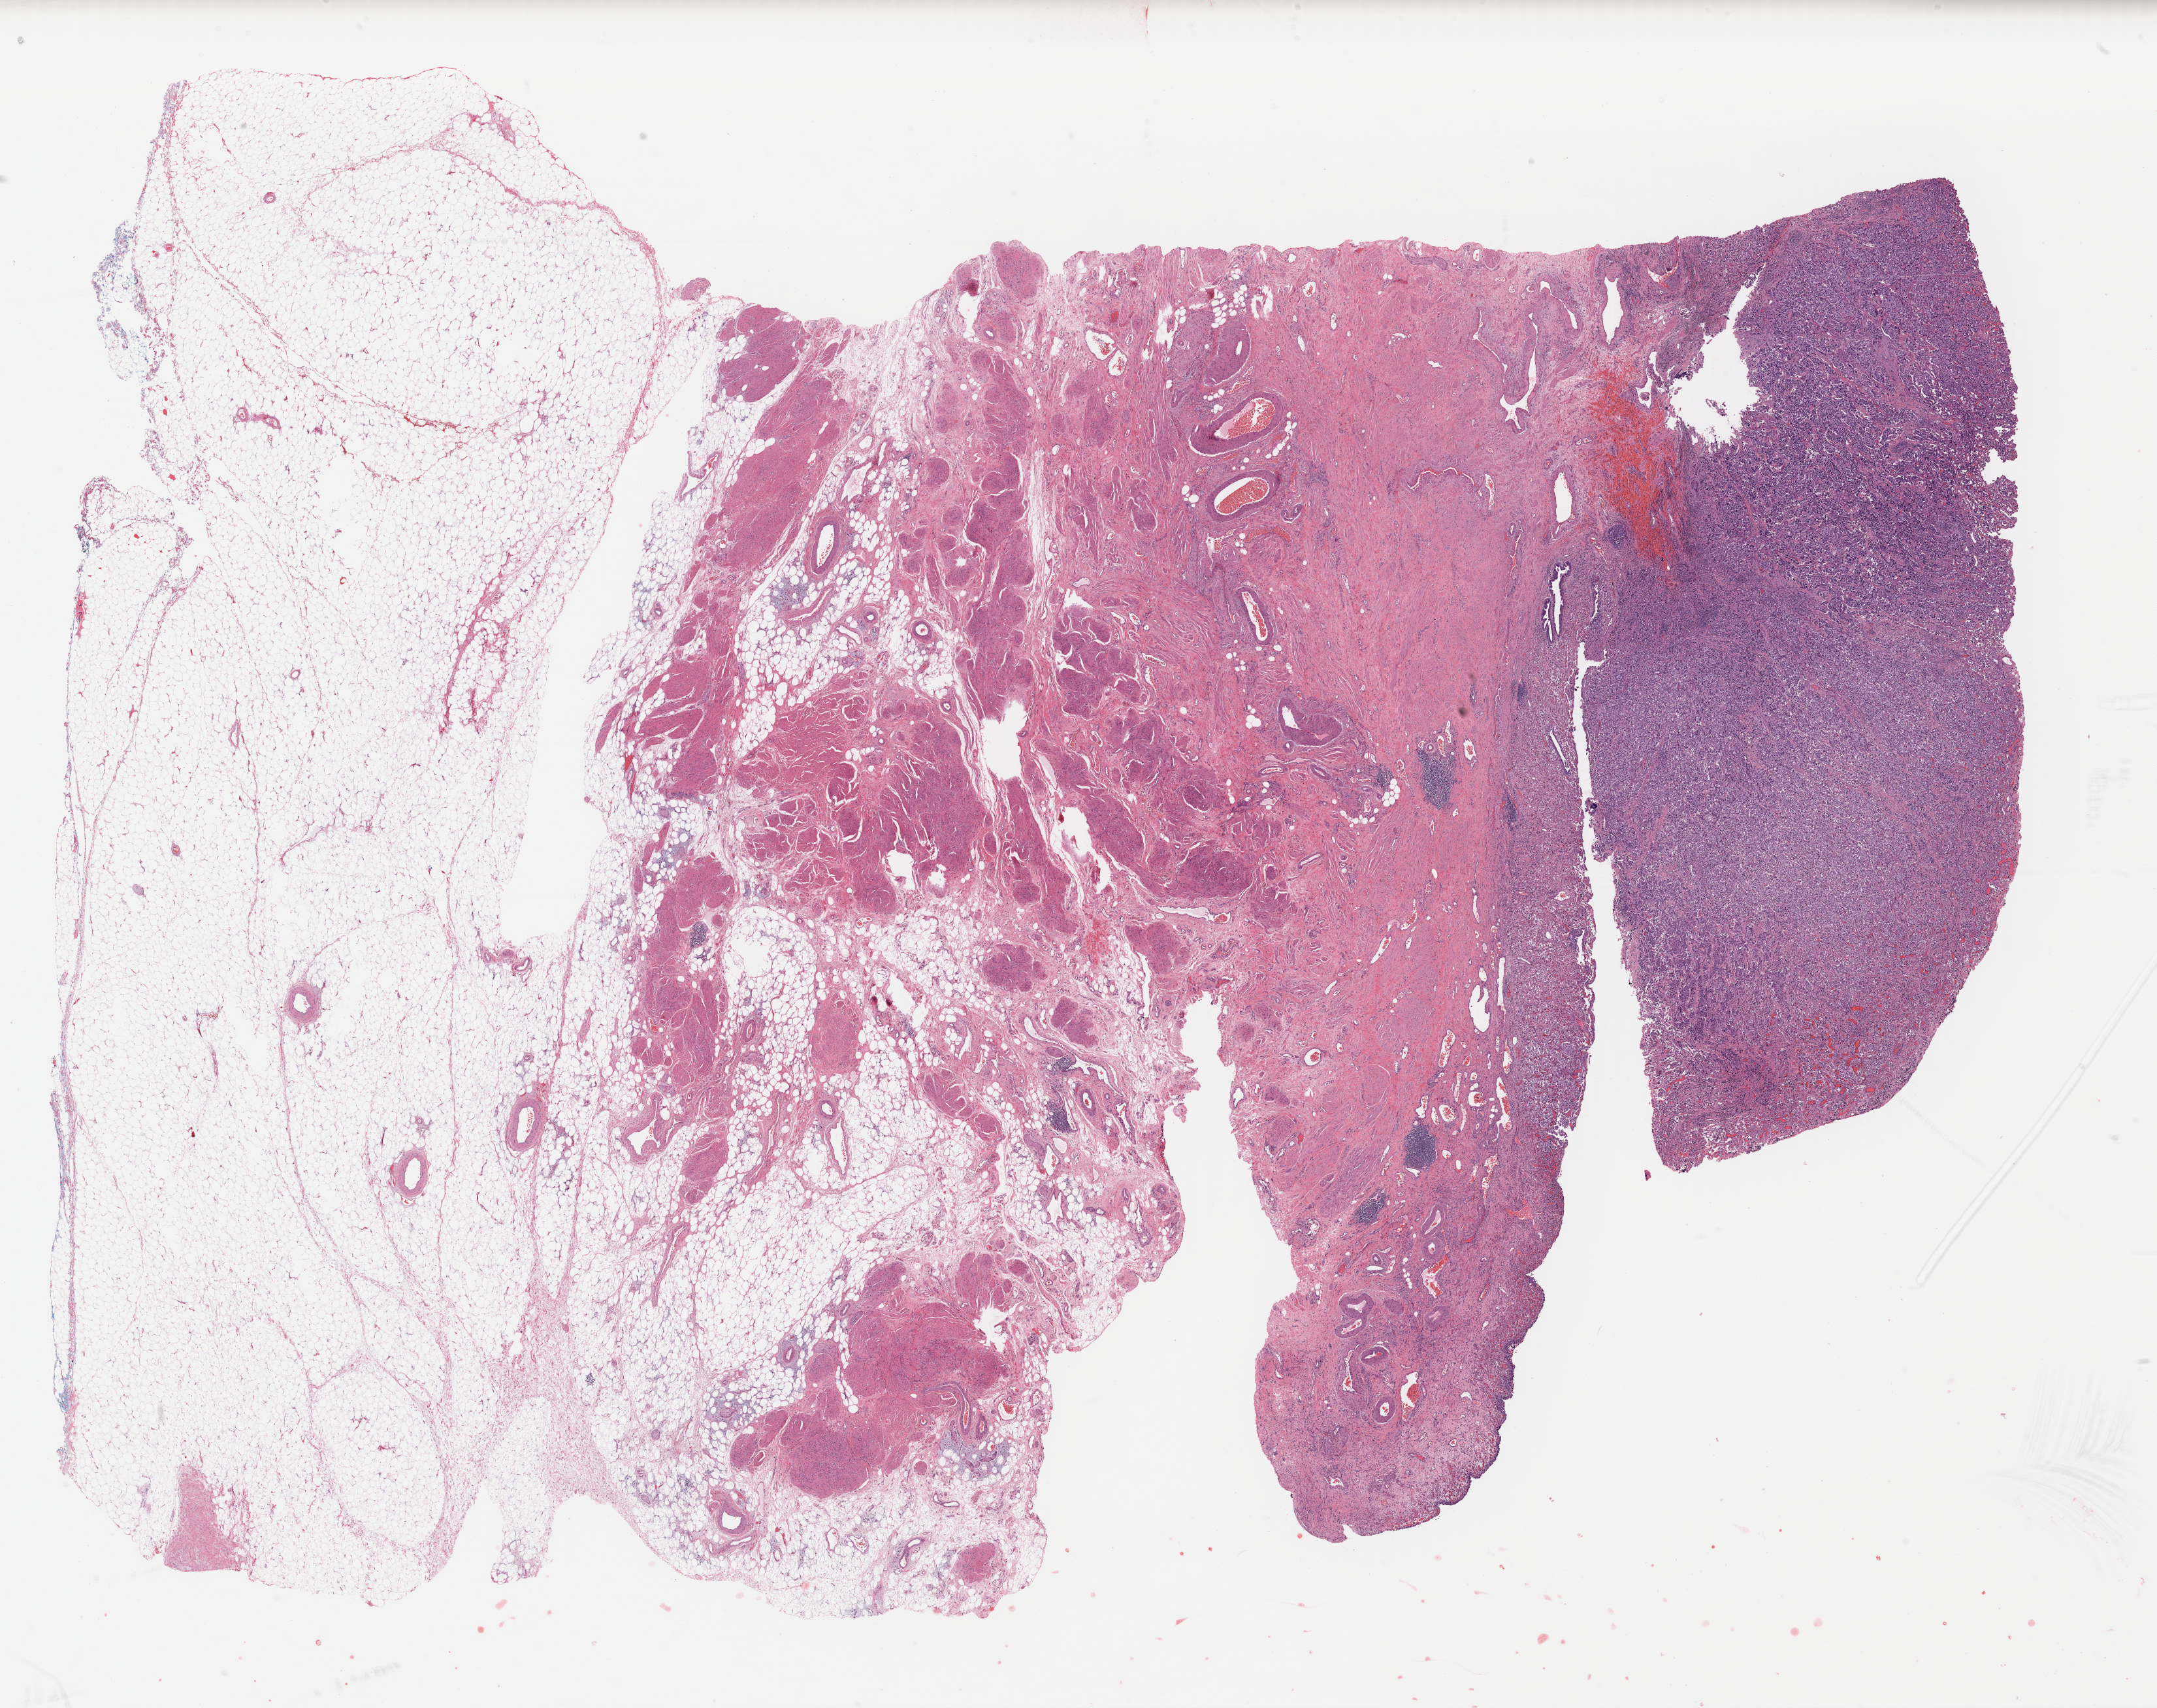
Digitized H&E-stained tissue section (whole slide) — shown as a low-resolution overview of the whole scanned area (about 26.0 x 20.6 mm, from a 40x scan). Formalin-fixed paraffin-embedded (FFPE) diagnostic section. Primary tumour sample from the bladder. Male, age 76 years at initial diagnosis.
Diagnosis: Transitional cell carcinoma.